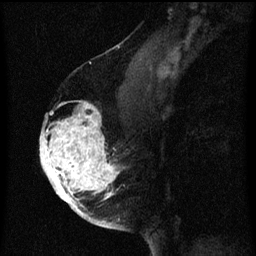
Breast MRI (dynamic contrast-enhanced), one sagittal slice; position 39 of 60 along the scan axis; dynamic contrast-enhanced series, image 2 of 3 at this slice position (ordered by acquisition); 1.5 T; TE 4.2 ms, TR 8 ms; 256 × 256 image matrix, field of view 180 × 180 mm. Female patient, age 56 years.
Annotated regions visible in this slice (semi-automatically segmented with operator editing):
- analysis volume of interest (the breast-tissue region the enhancement analysis was run in; not a lesion): bounding box <40,104,125,219> (left, top, right, bottom; pixels)
- tumour enhancement mask (voxels above the 70 % enhancement threshold inside the analysis volume of interest): <40,104,119,219>